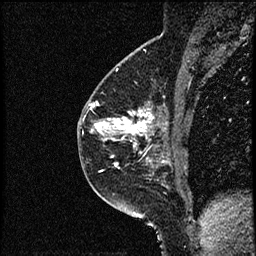
Breast MRI (dynamic contrast-enhanced), one sagittal slice; dynamic contrast-enhanced study with each time point stored as its own series, time point 2 of 3 at this slice position (early post-contrast, ordered by acquisition time); 1.5 T; TE 4.2 ms, TR 17.6 ms; 256 × 256 image matrix, field of view 200 × 200 mm. Female patient, age 49 years. From the clinical record (not read from this slice): setting: breast cancer imaged before/during neoadjuvant chemotherapy; receptor status: HER2-positive.
Structures marked on this image (semi-automatic segmentation, software-assisted and operator-edited):
- analysis volume of interest (the breast-tissue region the enhancement analysis was run in; not a lesion): bounding box [x1, y1, x2, y2] px = [85, 65, 182, 175]
- tumour enhancement mask (voxels above the 100 % enhancement threshold inside the analysis volume of interest): [91, 104, 166, 166]